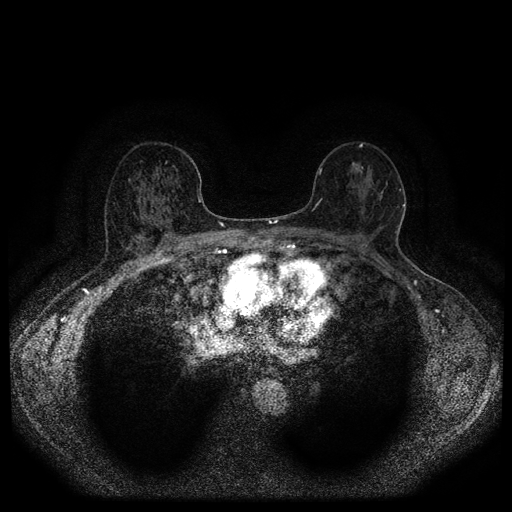
Breast MRI (dynamic contrast-enhanced, multi-phase), one axial slice. Slice 62 of 116 in the series (ordered by position). Dynamic contrast-enhanced series, time point 2 of 5 at this slice position (early post-contrast). 1.5 T. TE 2.7 ms, TR 5.4 ms. 512 × 512 image matrix, field of view 330 × 330 mm. Female patient, age 56 years.
Structures marked on this image (semi-automatic segmentation, software-assisted and operator-edited):
- breast lesion (labelled 'tumour' in the annotation; benign lesions carry a separate 'benign' label): bounding box <380,181,388,198> (left, top, right, bottom; pixels)